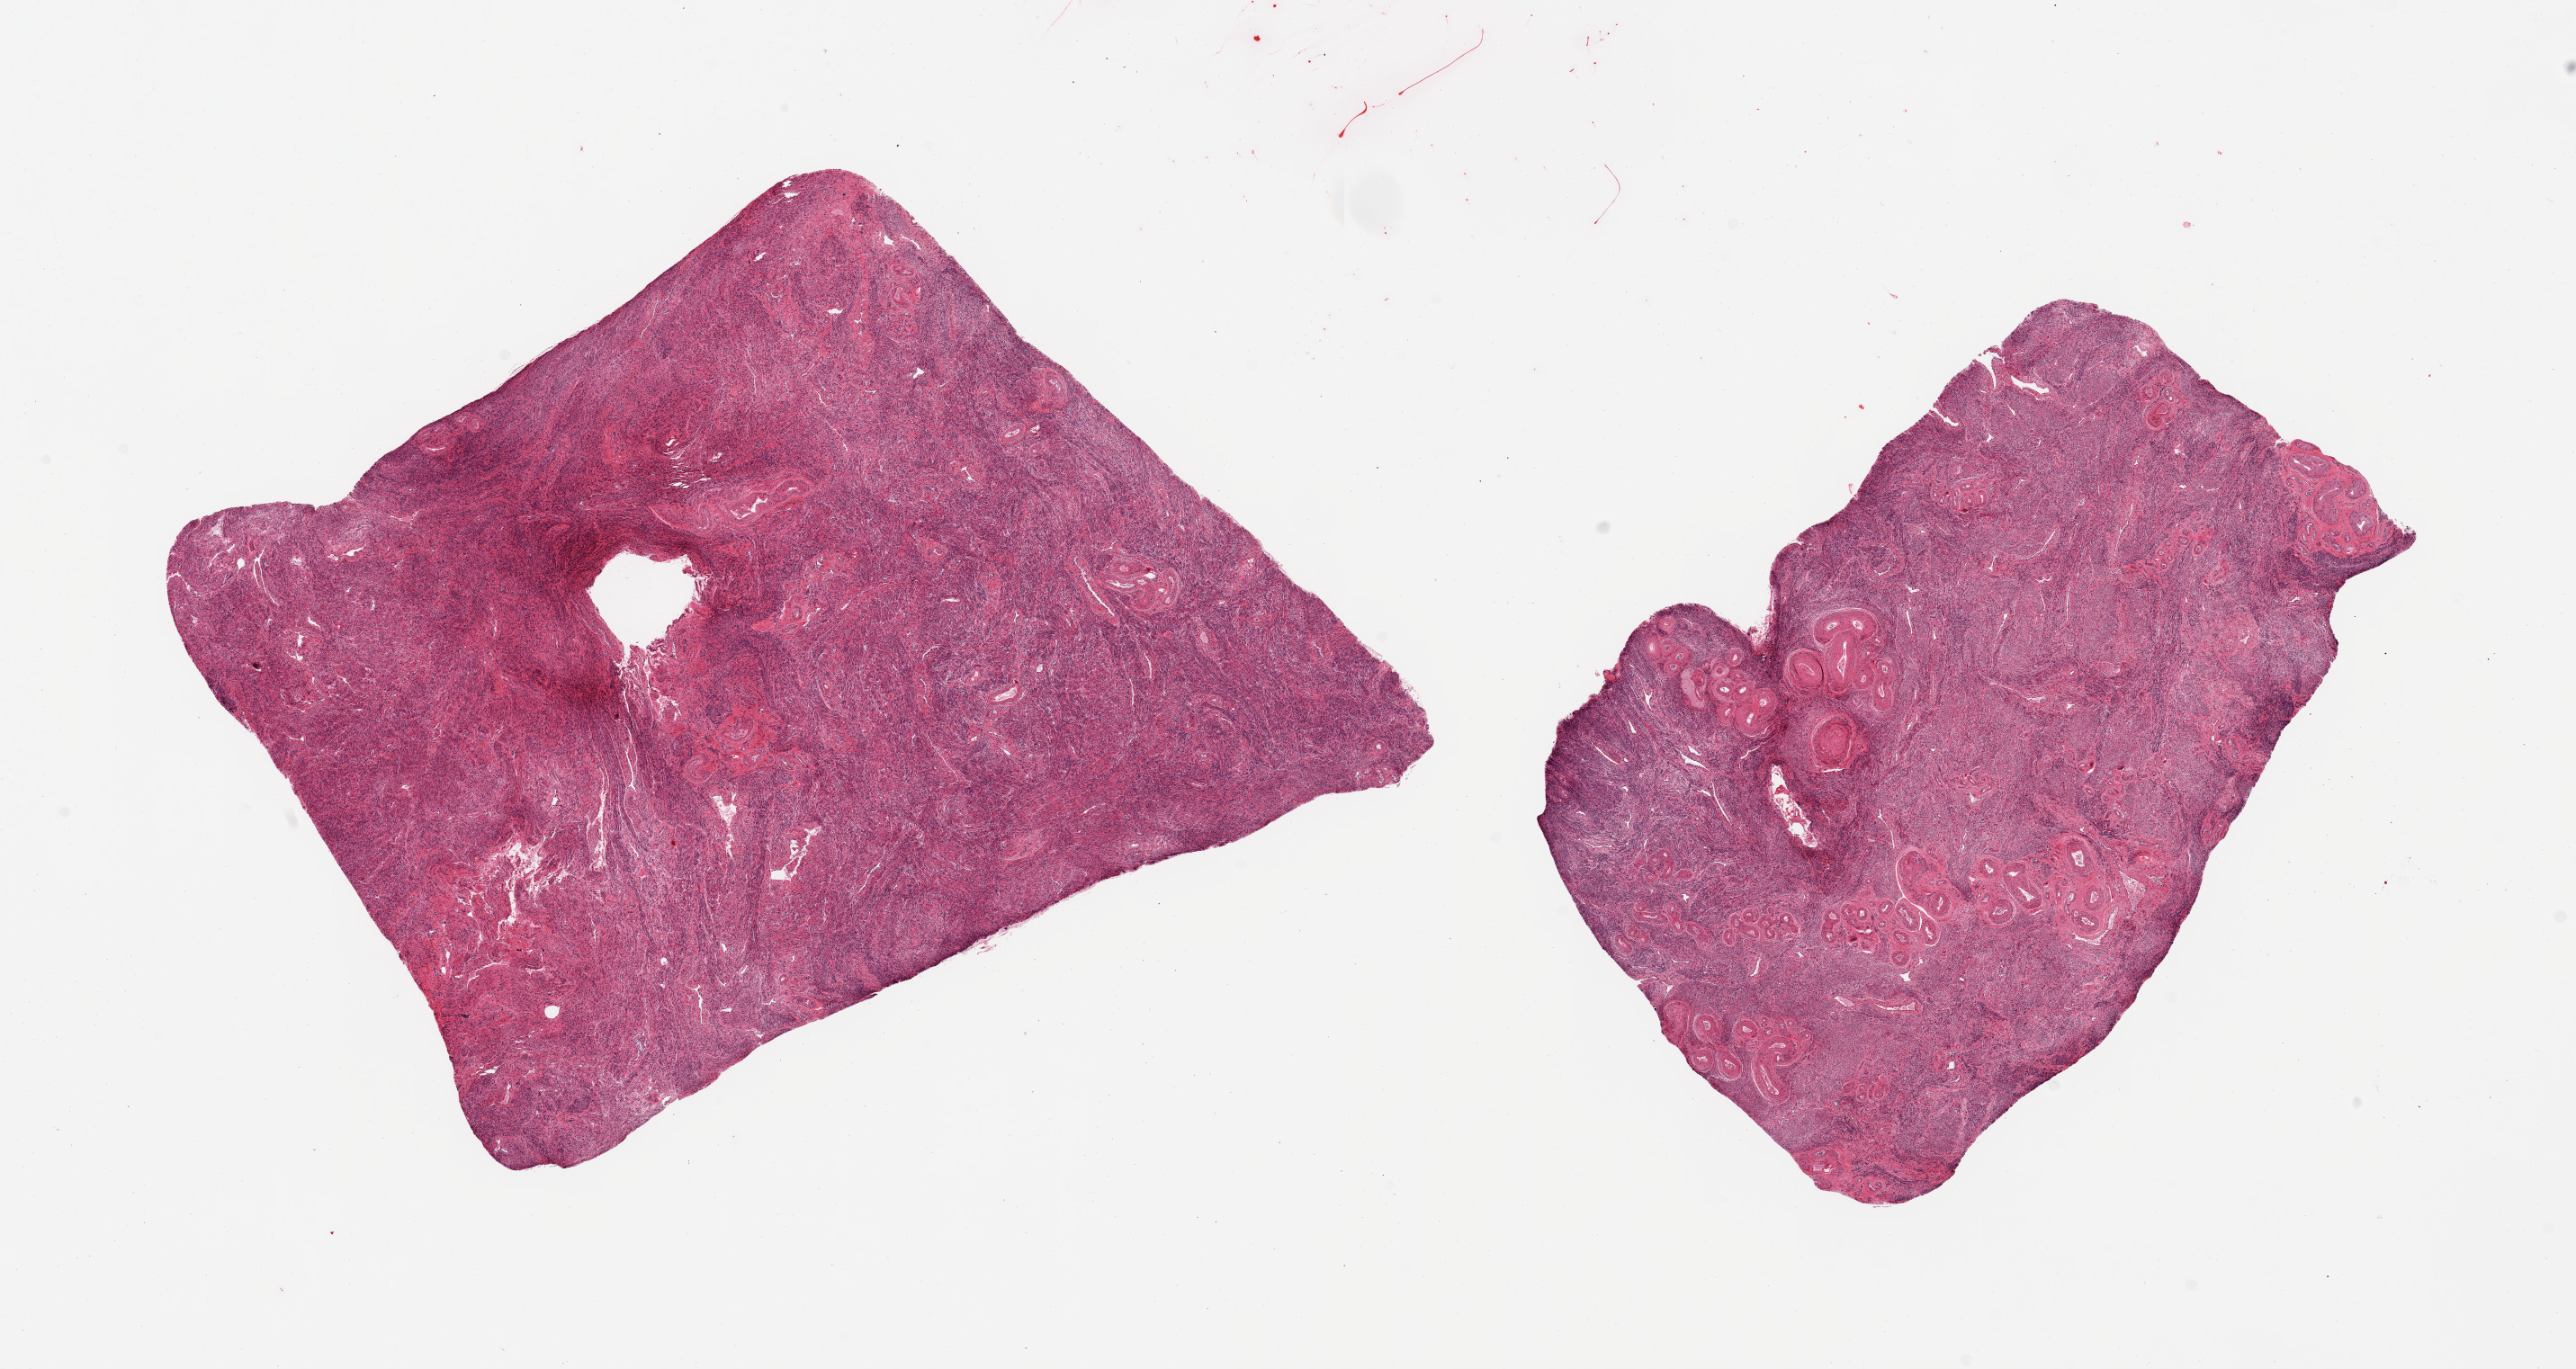
Digitized haematoxylin and eosin-stained section — shown as a low-resolution overview of the whole scanned area (about 22.6 x 12.0 mm); PAXgene-fixed, paraffin-embedded tissue; target tissue: uterus; donor tissue sample. Donor: female.
Review note (as recorded): 2 pieces, myometrium, no endometrium.